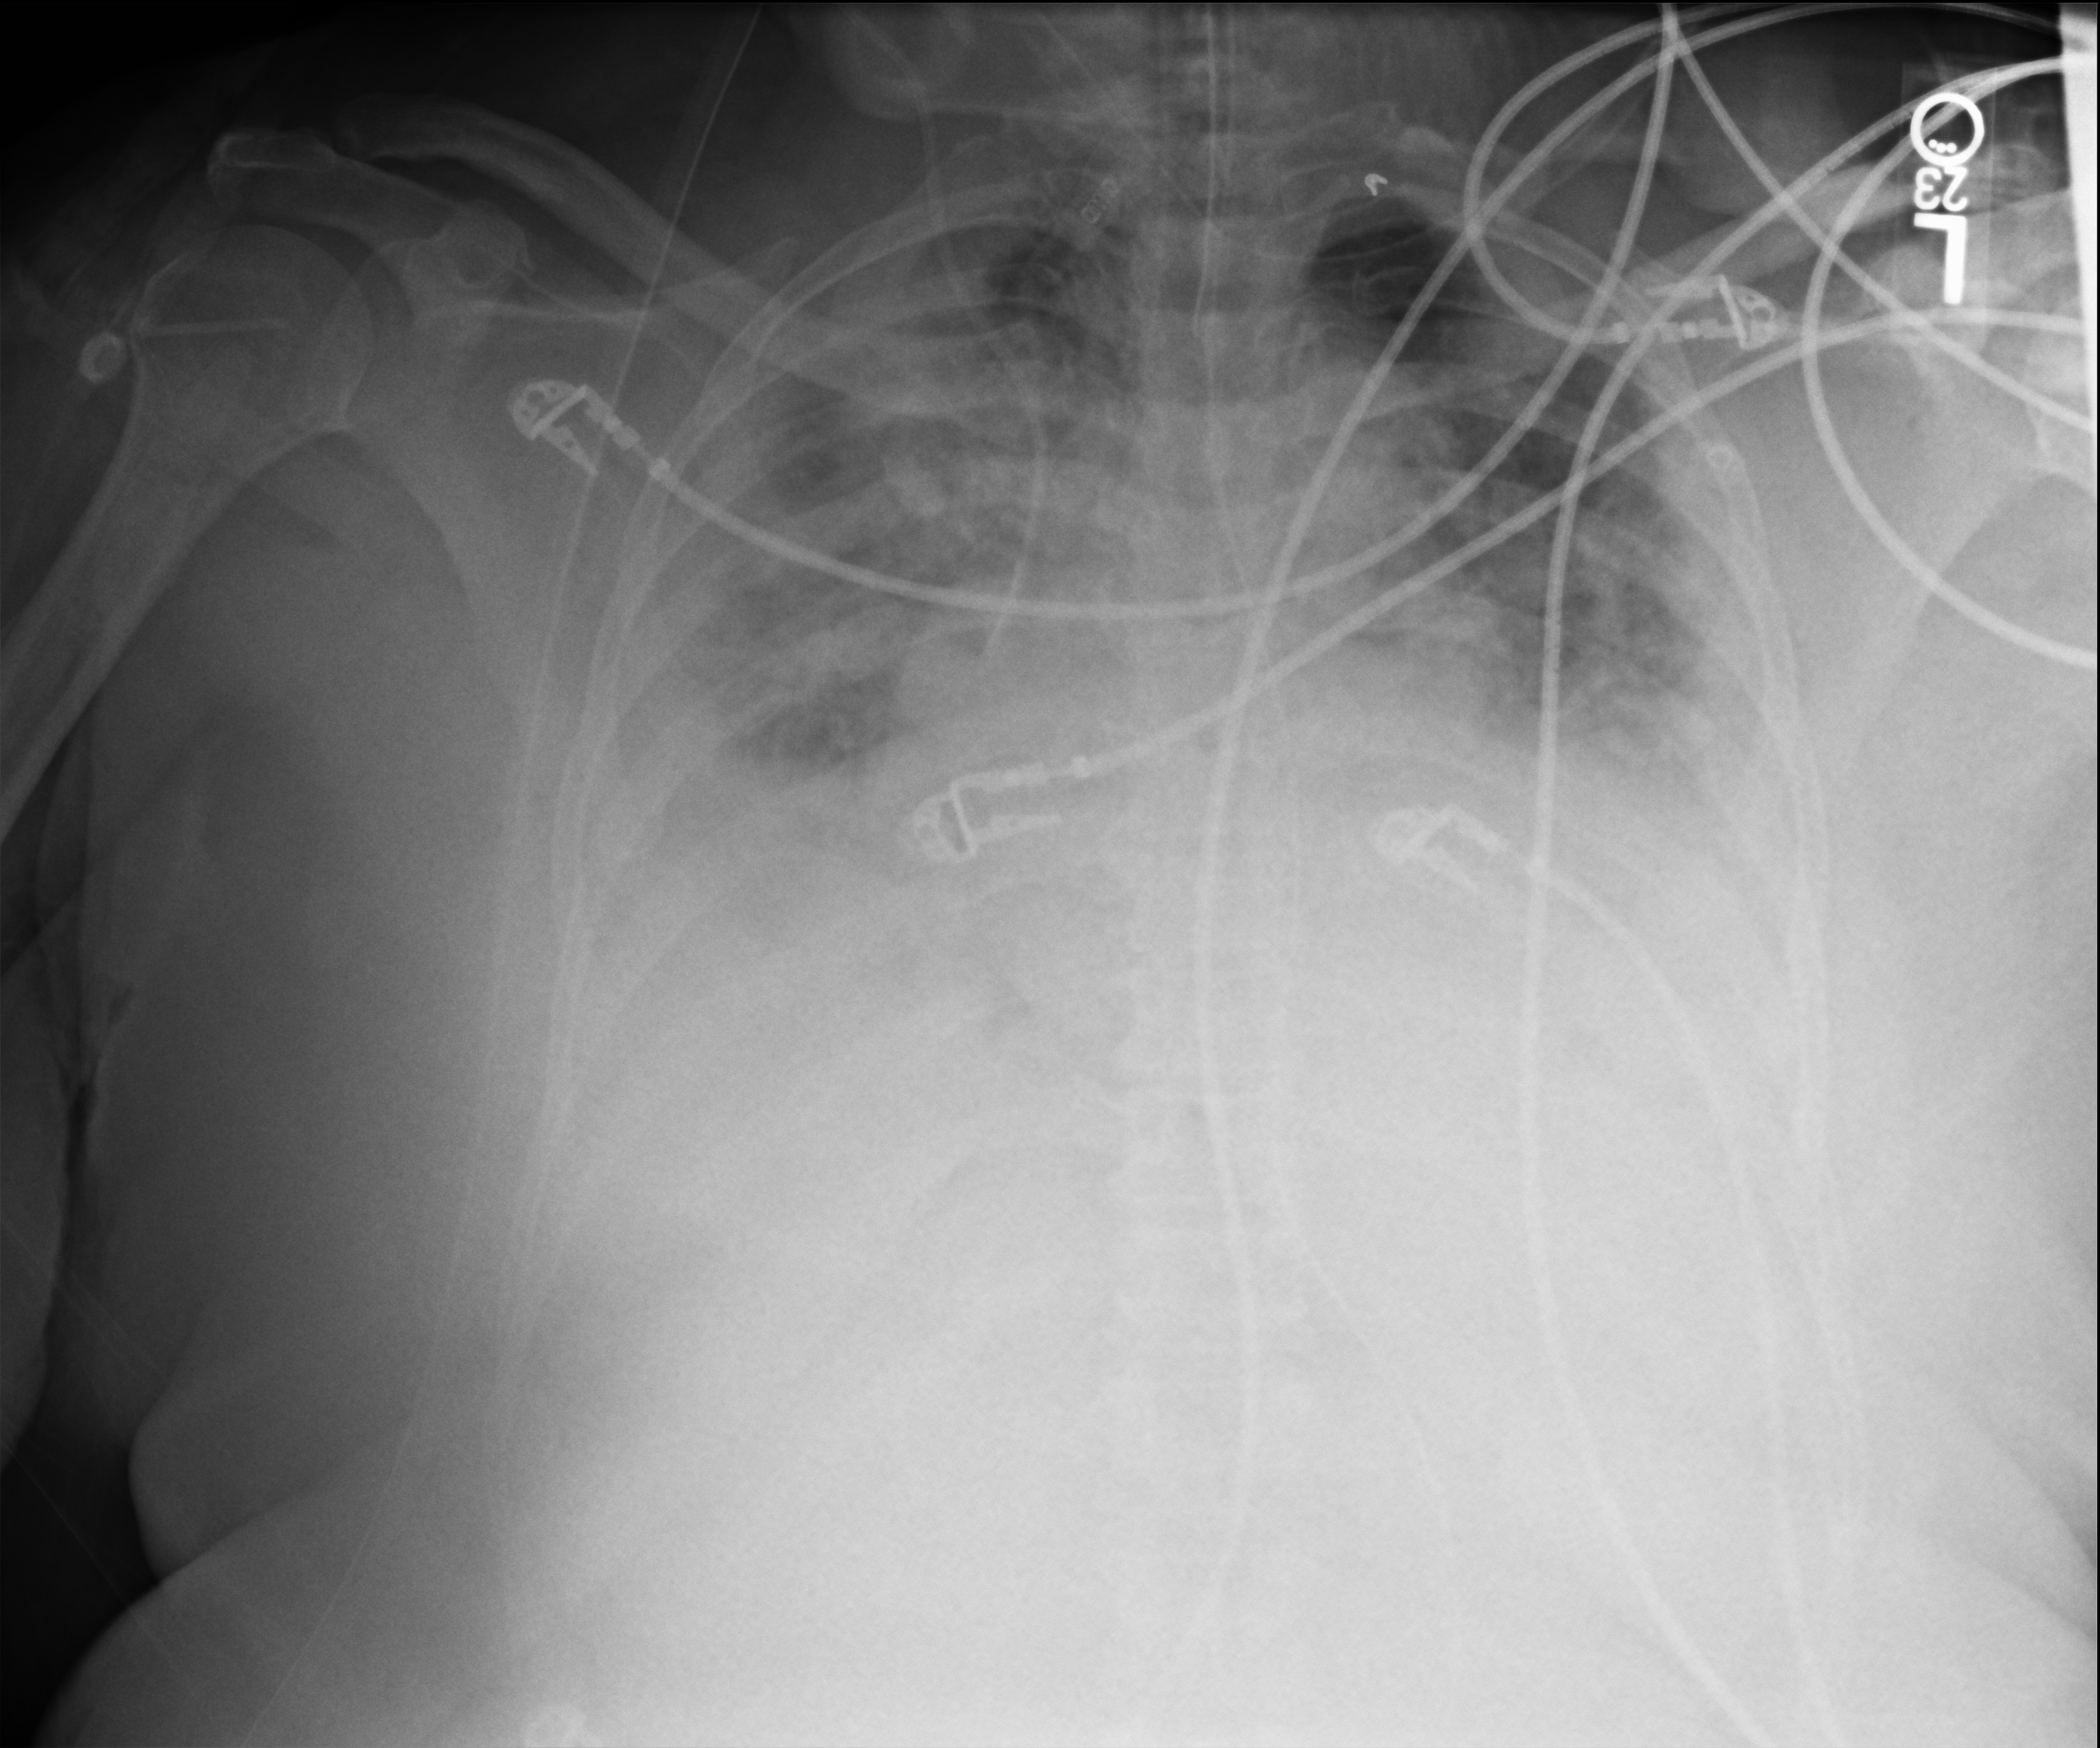
Chest X-ray (portable); anteroposterior (AP) projection. Female patient hospitalised with COVID-19, age 60–74 years.
Admission-level facts for this patient (not findings on this image; timing relative to this image not recorded): length of hospital stay: 9 days.